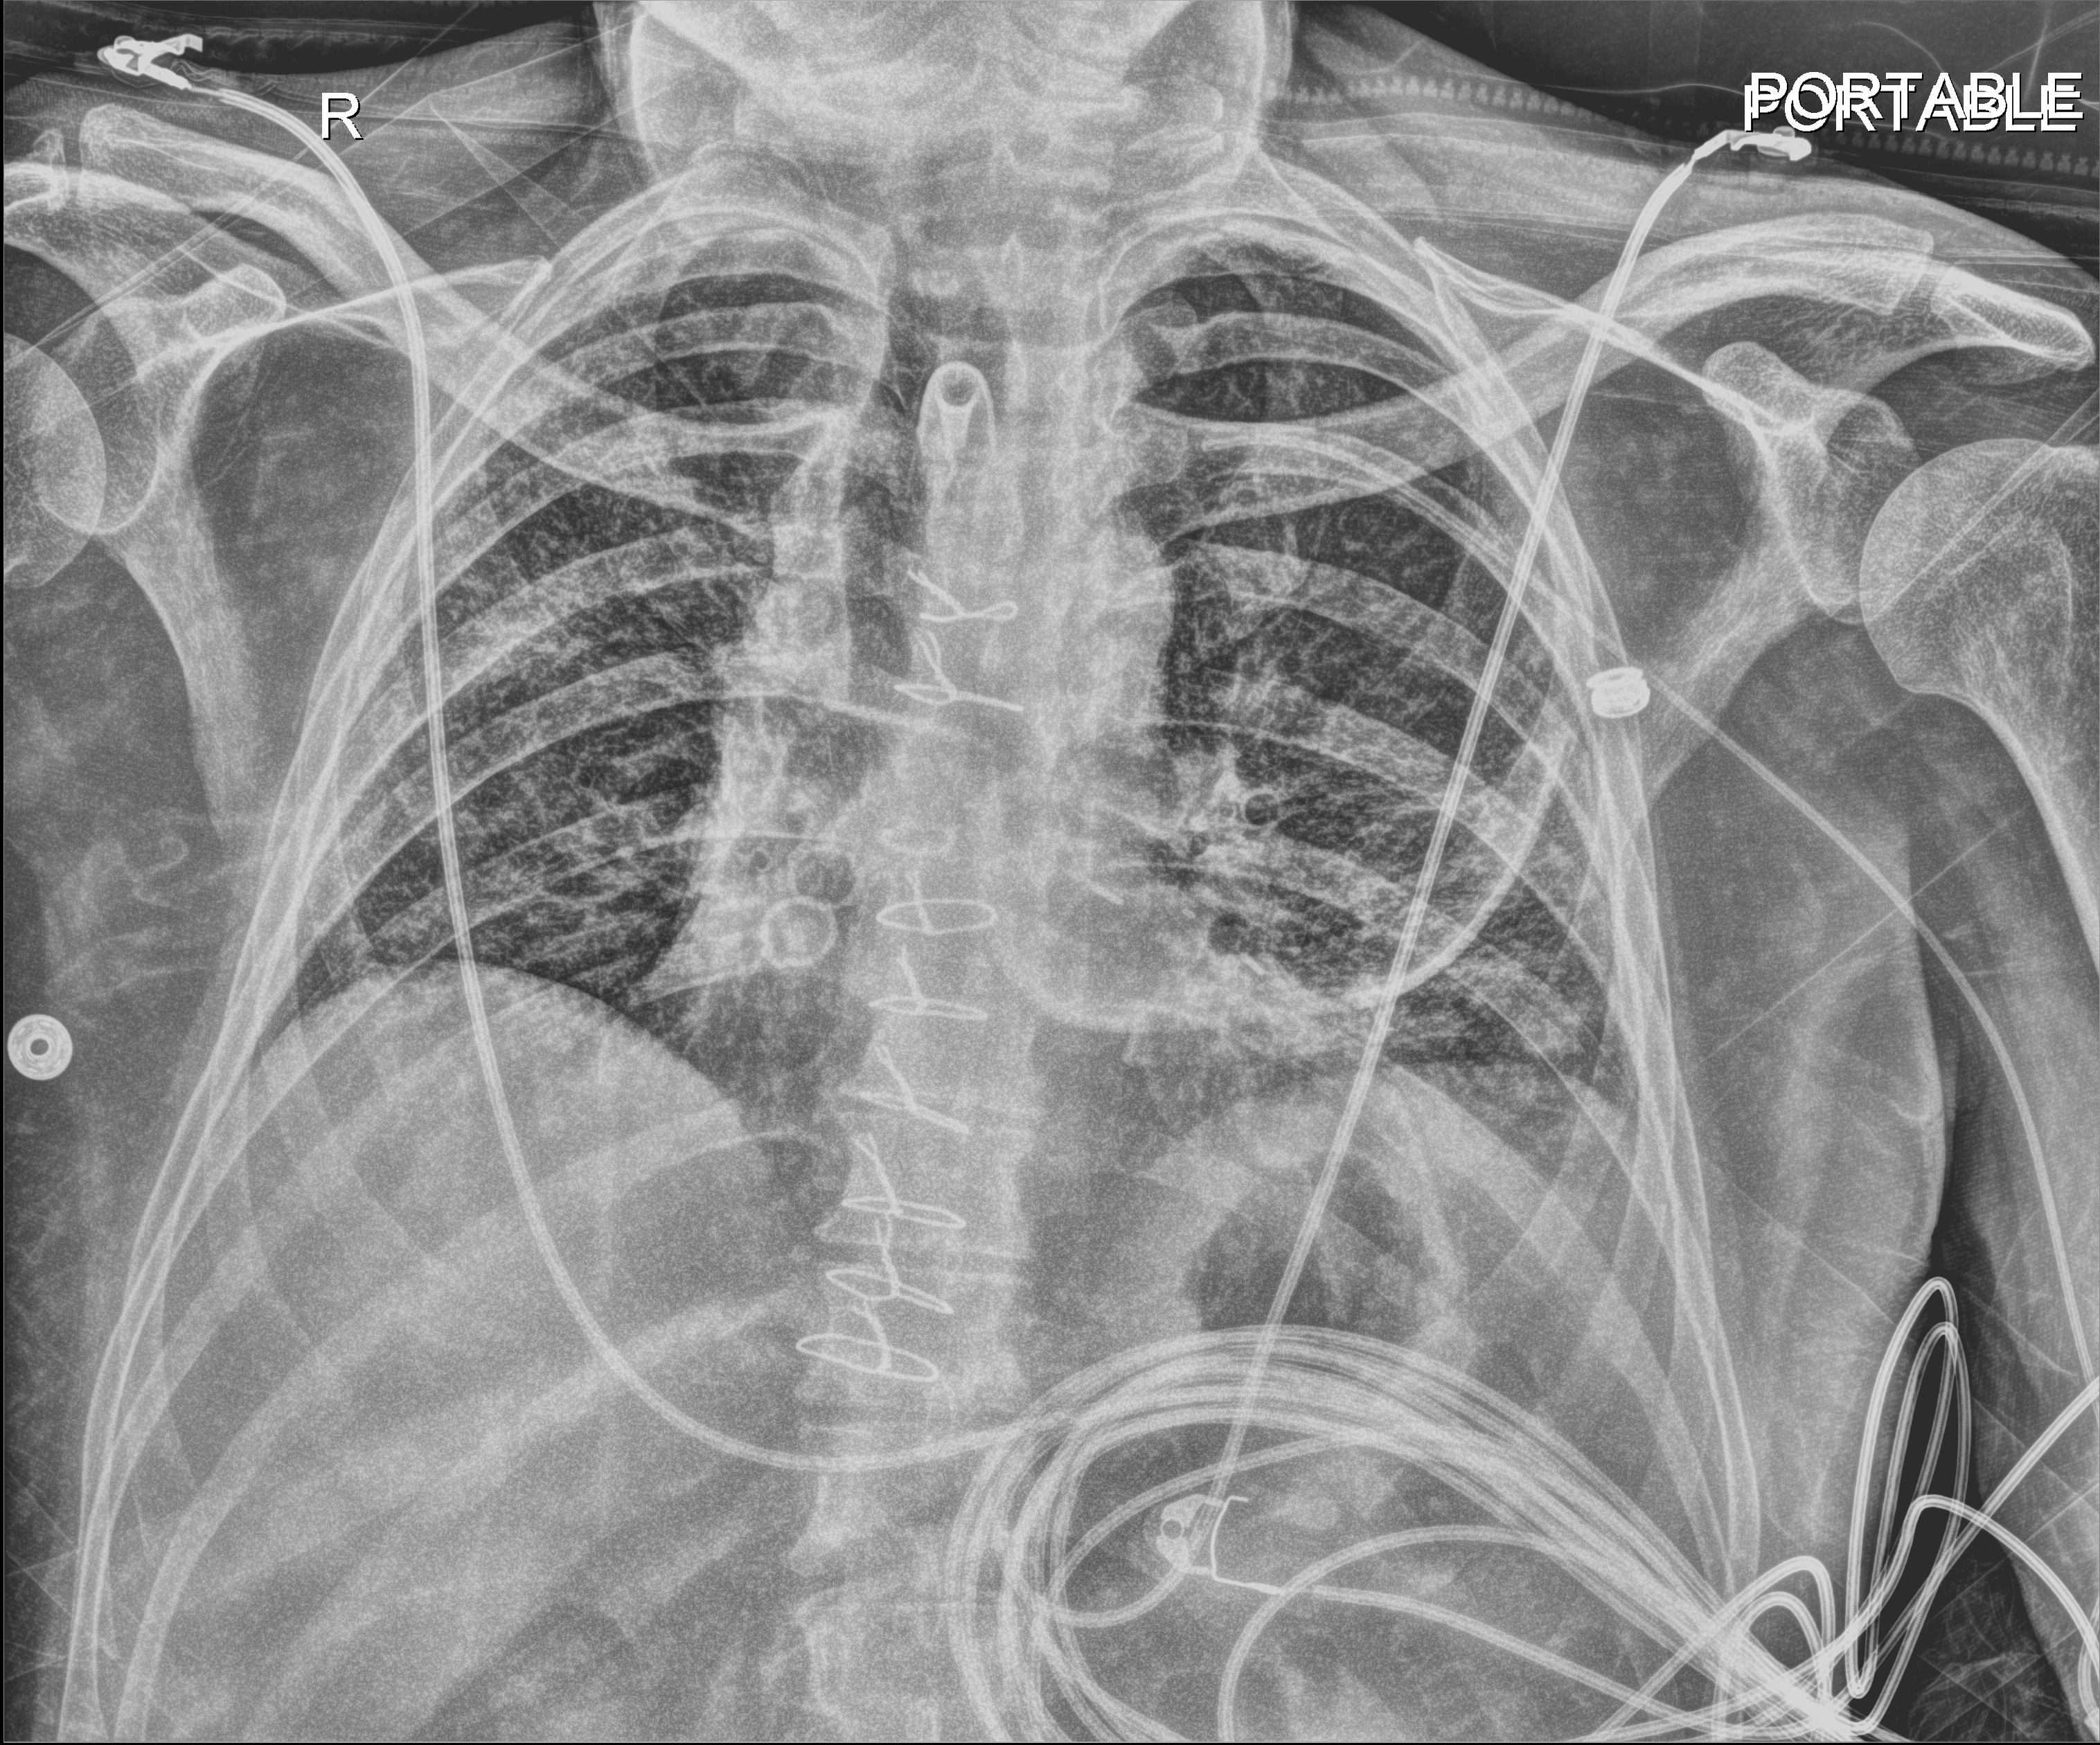
Bedside chest radiograph (digital radiography). Patient hospitalised with COVID-19; male, aged 18–59 years.
Hospital-stay facts (about this admission, not read from this image; timing relative to this image not recorded): diabetes (admission record): yes; admitted to intensive care during this hospital stay: yes; mechanically ventilated during this hospital stay: yes.